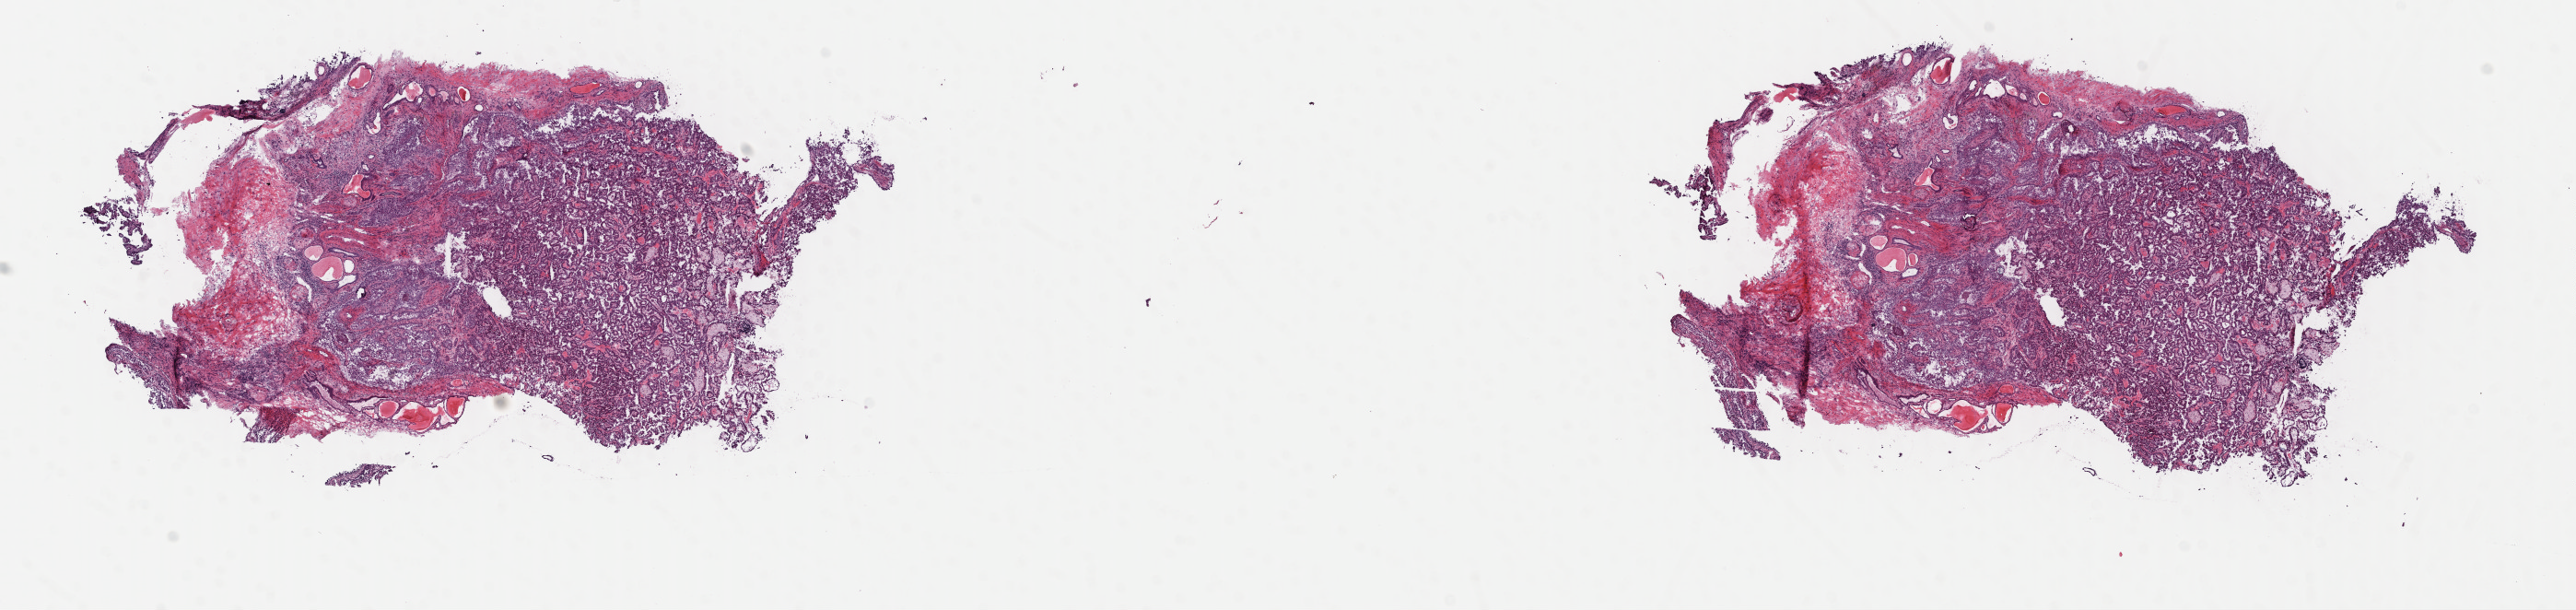
Hematoxylin and eosin (H&E) stained whole-slide image — whole scanned area (about 22.0 x 5.2 mm) shown as a low-resolution overview; frozen section; sample: primary tumour, kidney. Male, age 77 years at initial diagnosis. Pathologist review of this section (percent, as recorded): tumour cells 100%, tumour nuclei 65%, normal cells 0%, stromal cells 0%, necrosis 0%. Inflammatory infiltration, as recorded: lymphocyte infiltration 2%, monocyte infiltration 0%, neutrophil infiltration 0%.
* AJCC pathologic stage: I (7th edition)
* laterality: left
* histologic diagnosis: Papillary adenocarcinoma, NOS